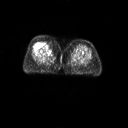
FDG PET of an extremity soft-tissue mass (from a PET/CT study), one axial slice. Slice 18 of 267 in the series (ordered by position). 128 × 128 image matrix. Patient: female, 56 years. From the clinical record (not read from this slice): histological type: malignant solitary fibrous tumor; grade: intermediate; site of the primary tumour: right thigh.
Outlined on this slice (expert contour drawn on MRI and transferred to this co-registered scan by the dataset authors):
- gross tumour volume including surrounding oedema: bounding box <40,41,52,49> (left, top, right, bottom; pixels)